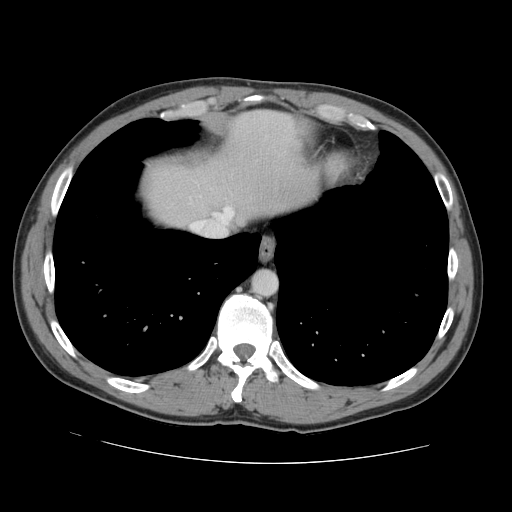
Contrast-enhanced abdominal CT, one axial slice; position 126 of 131 along the scan axis; intravenous contrast given; soft-tissue window (W 400 / L 40 HU); 512 × 512 image matrix. Male patient, age 40 years. Case-level facts recorded for this patient, not image findings: diagnosis: colorectal cancer liver metastases, imaged before liver resection; multiple liver metastases: yes; largest metastasis: 2.9 cm; chemotherapy before resection: yes.
Annotated regions visible in this slice (expert manual segmentation):
- hepatic veins: bounding box (x1, y1, x2, y2) in pixels: (191, 207, 233, 235)
- liver: (145, 112, 309, 225)
- planned liver remnant (the part of the liver to remain after resection): (146, 111, 310, 226)